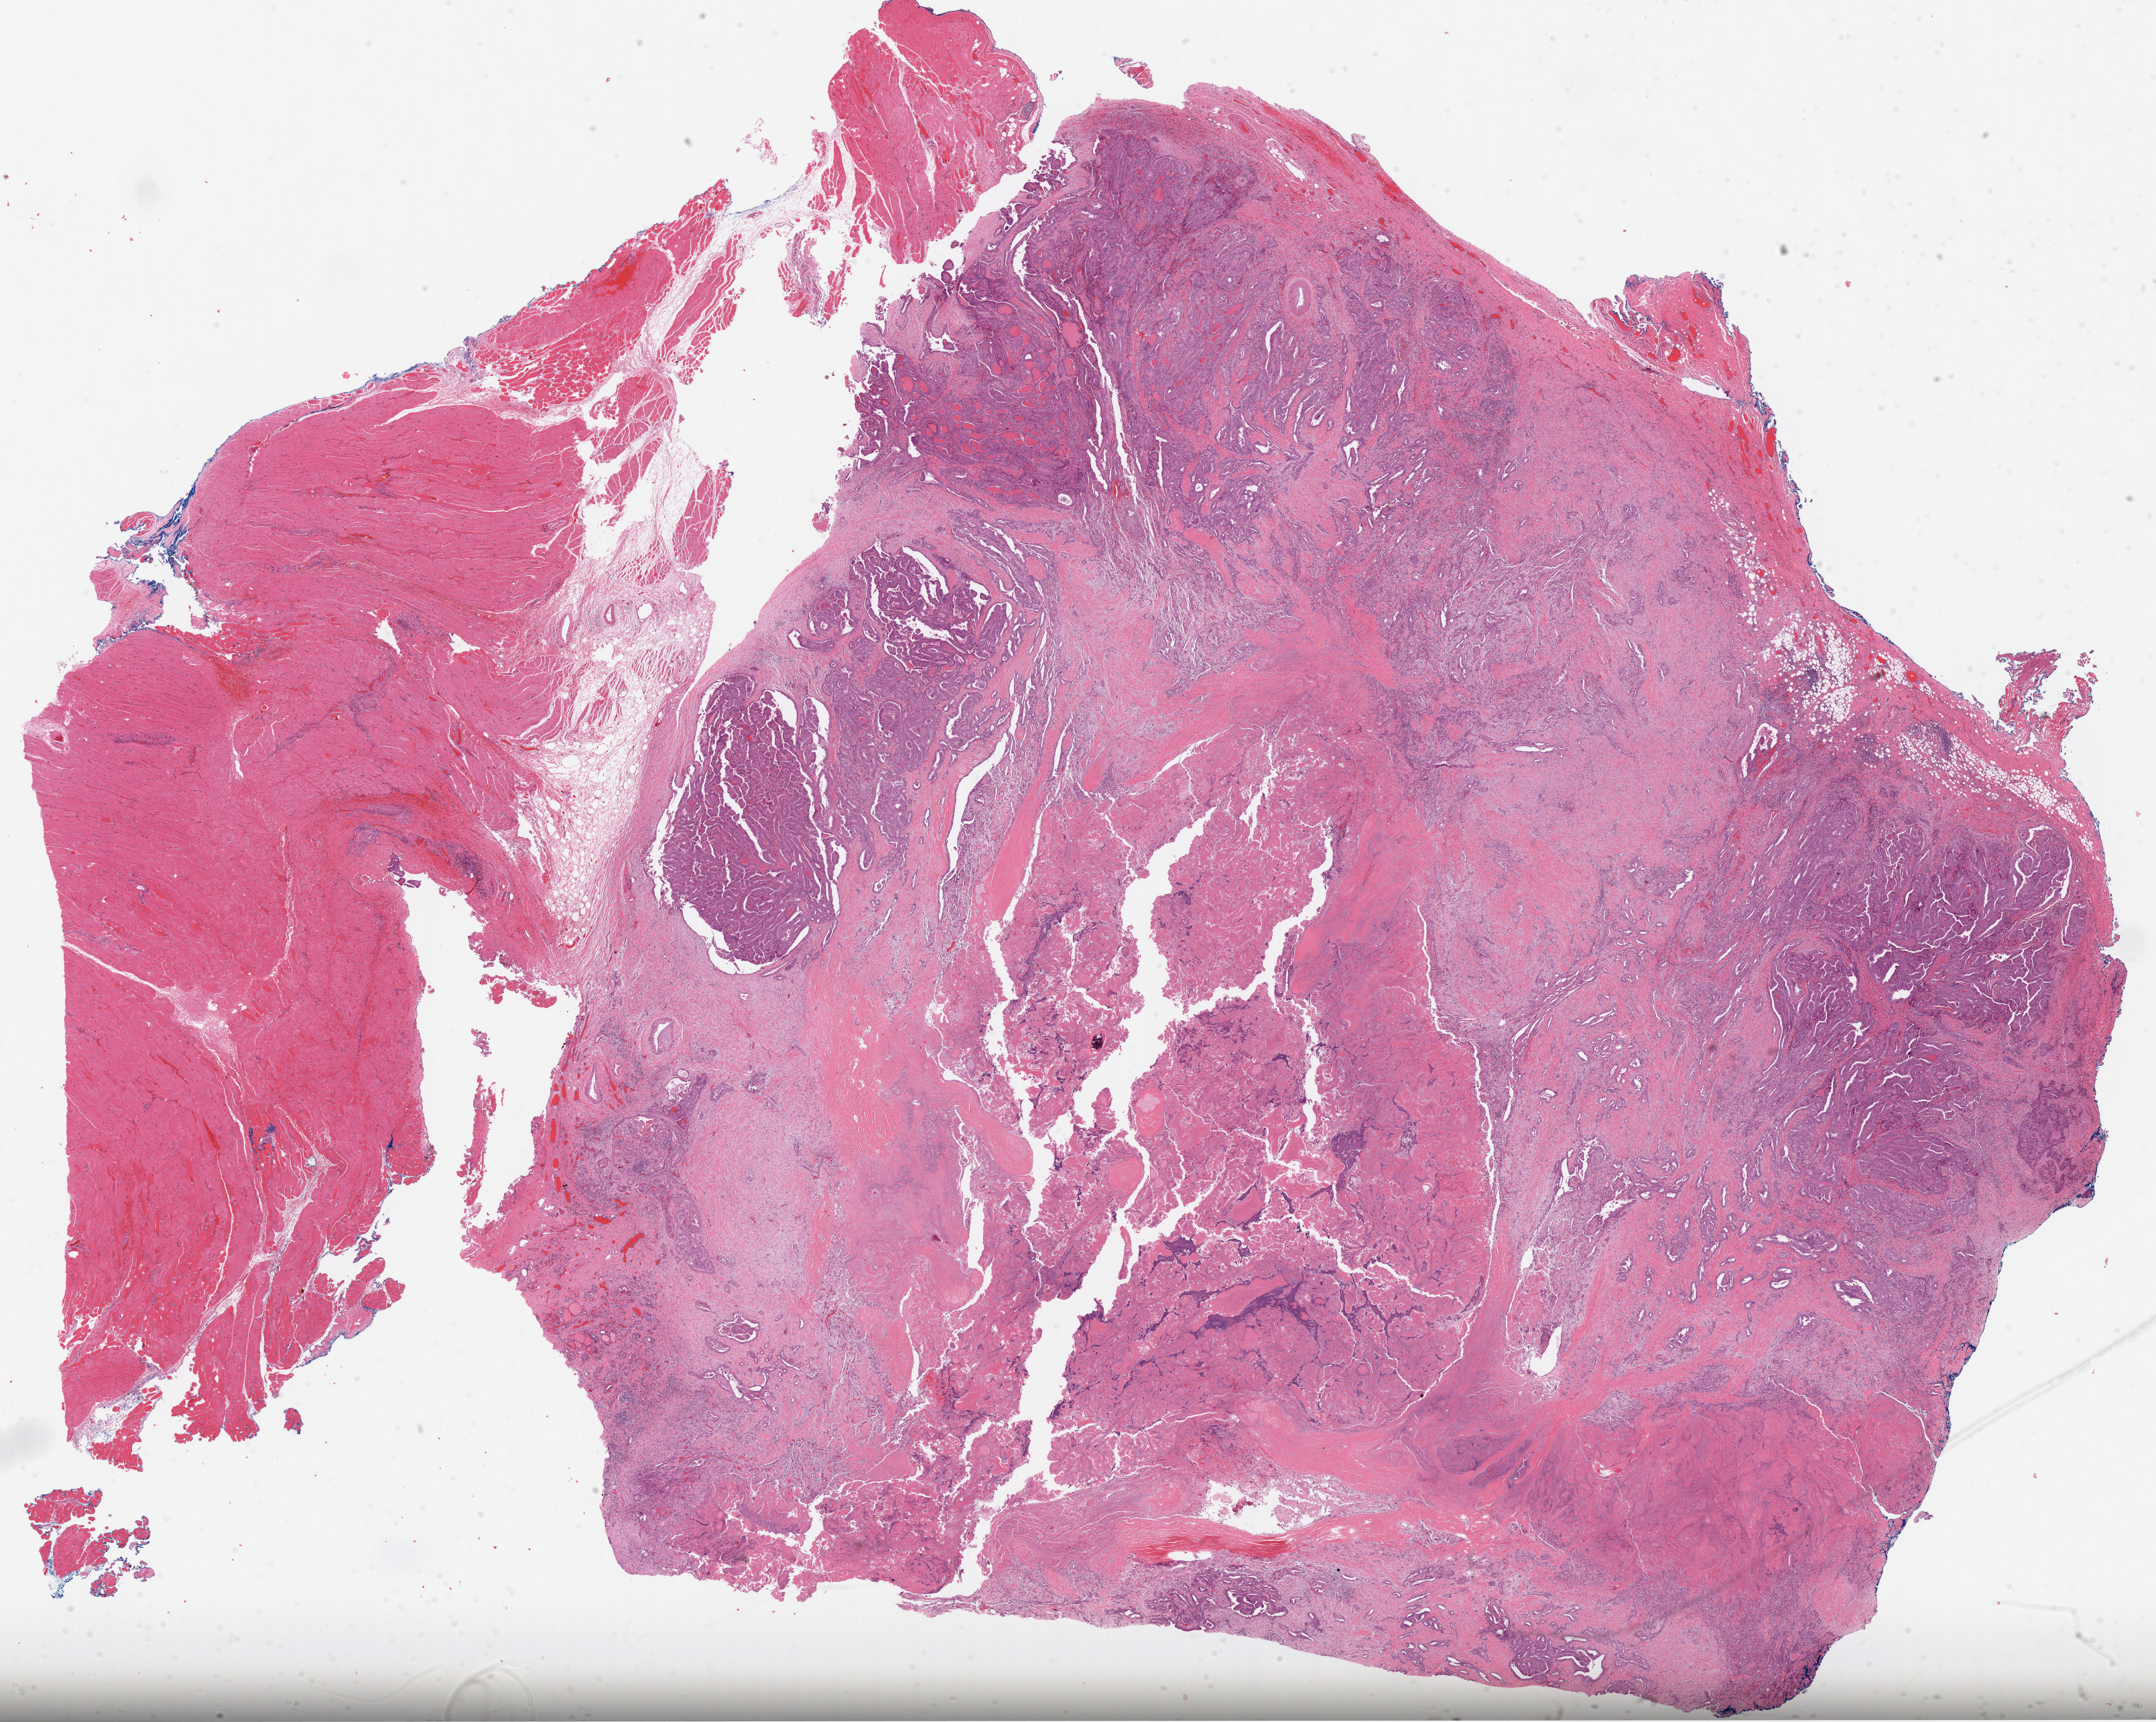
Digitized Hematoxylin and eosin (H&E) stained tissue section (whole slide) — a low-resolution overview of the entire scanned area, about 25.9 x 20.7 mm (slide scanned at 40x); formalin-fixed paraffin-embedded (FFPE) diagnostic section; sample: primary tumour, thyroid. Female, age 61 years at initial diagnosis.
- lymph nodes positive (case pathology): 0 of 6 examined
- AJCC pathologic stage: III
- histologic diagnosis: Papillary adenocarcinoma, NOS (thyroid gland)
- laterality: right